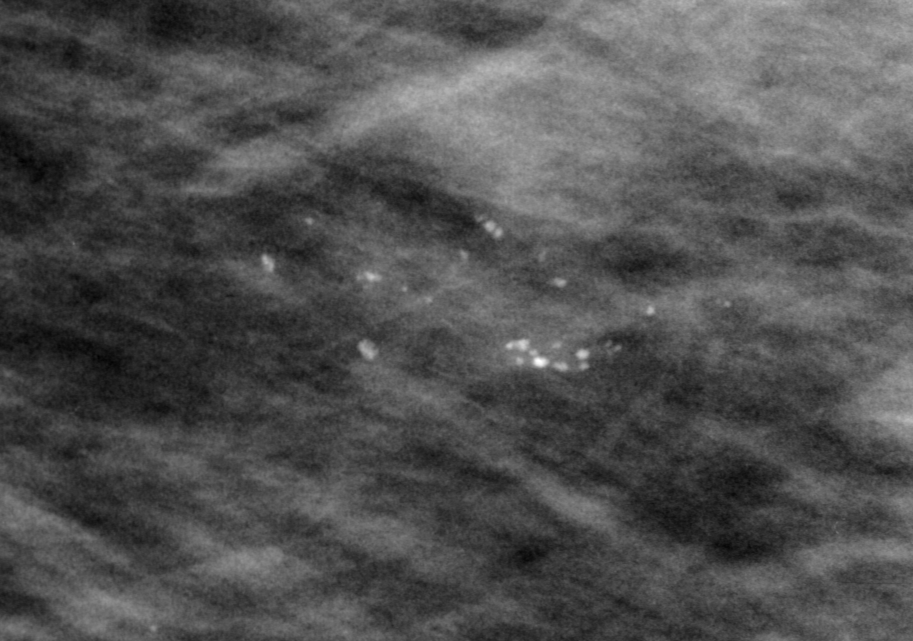
Crop from a digitized film mammogram around one marked abnormality; left breast; MLO view; BI-RADS breast density category 2 (scale 1–4).
- Finding: calcifications, morphology round and regular / pleomorphic, distribution clustered; BI-RADS assessment category 0 (incomplete: needs additional imaging); subtlety rating 4 on a 1 (subtle) to 5 (obvious) scale; pathology (as recorded): benign.